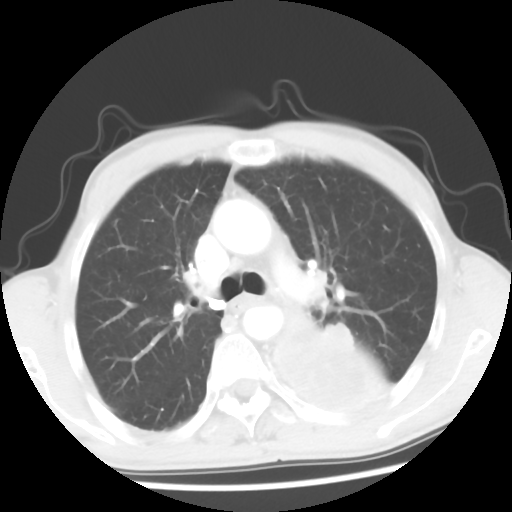
Chest CT, one axial slice; slice 38 of 56 in the series (ordered by position); lung window (W 1500 / L -600 HU); 512 × 512 image matrix. Patient: male, 60 years. Case-level facts recorded for this patient, not image findings: clinical TNM (as recorded): T4 N0 M0.
Outlined on this slice (rectangle marked by the reading radiologist):
- lung tumour (recorded histology: squamous cell carcinoma): bounding box <269,315,393,418> (left, top, right, bottom; pixels)